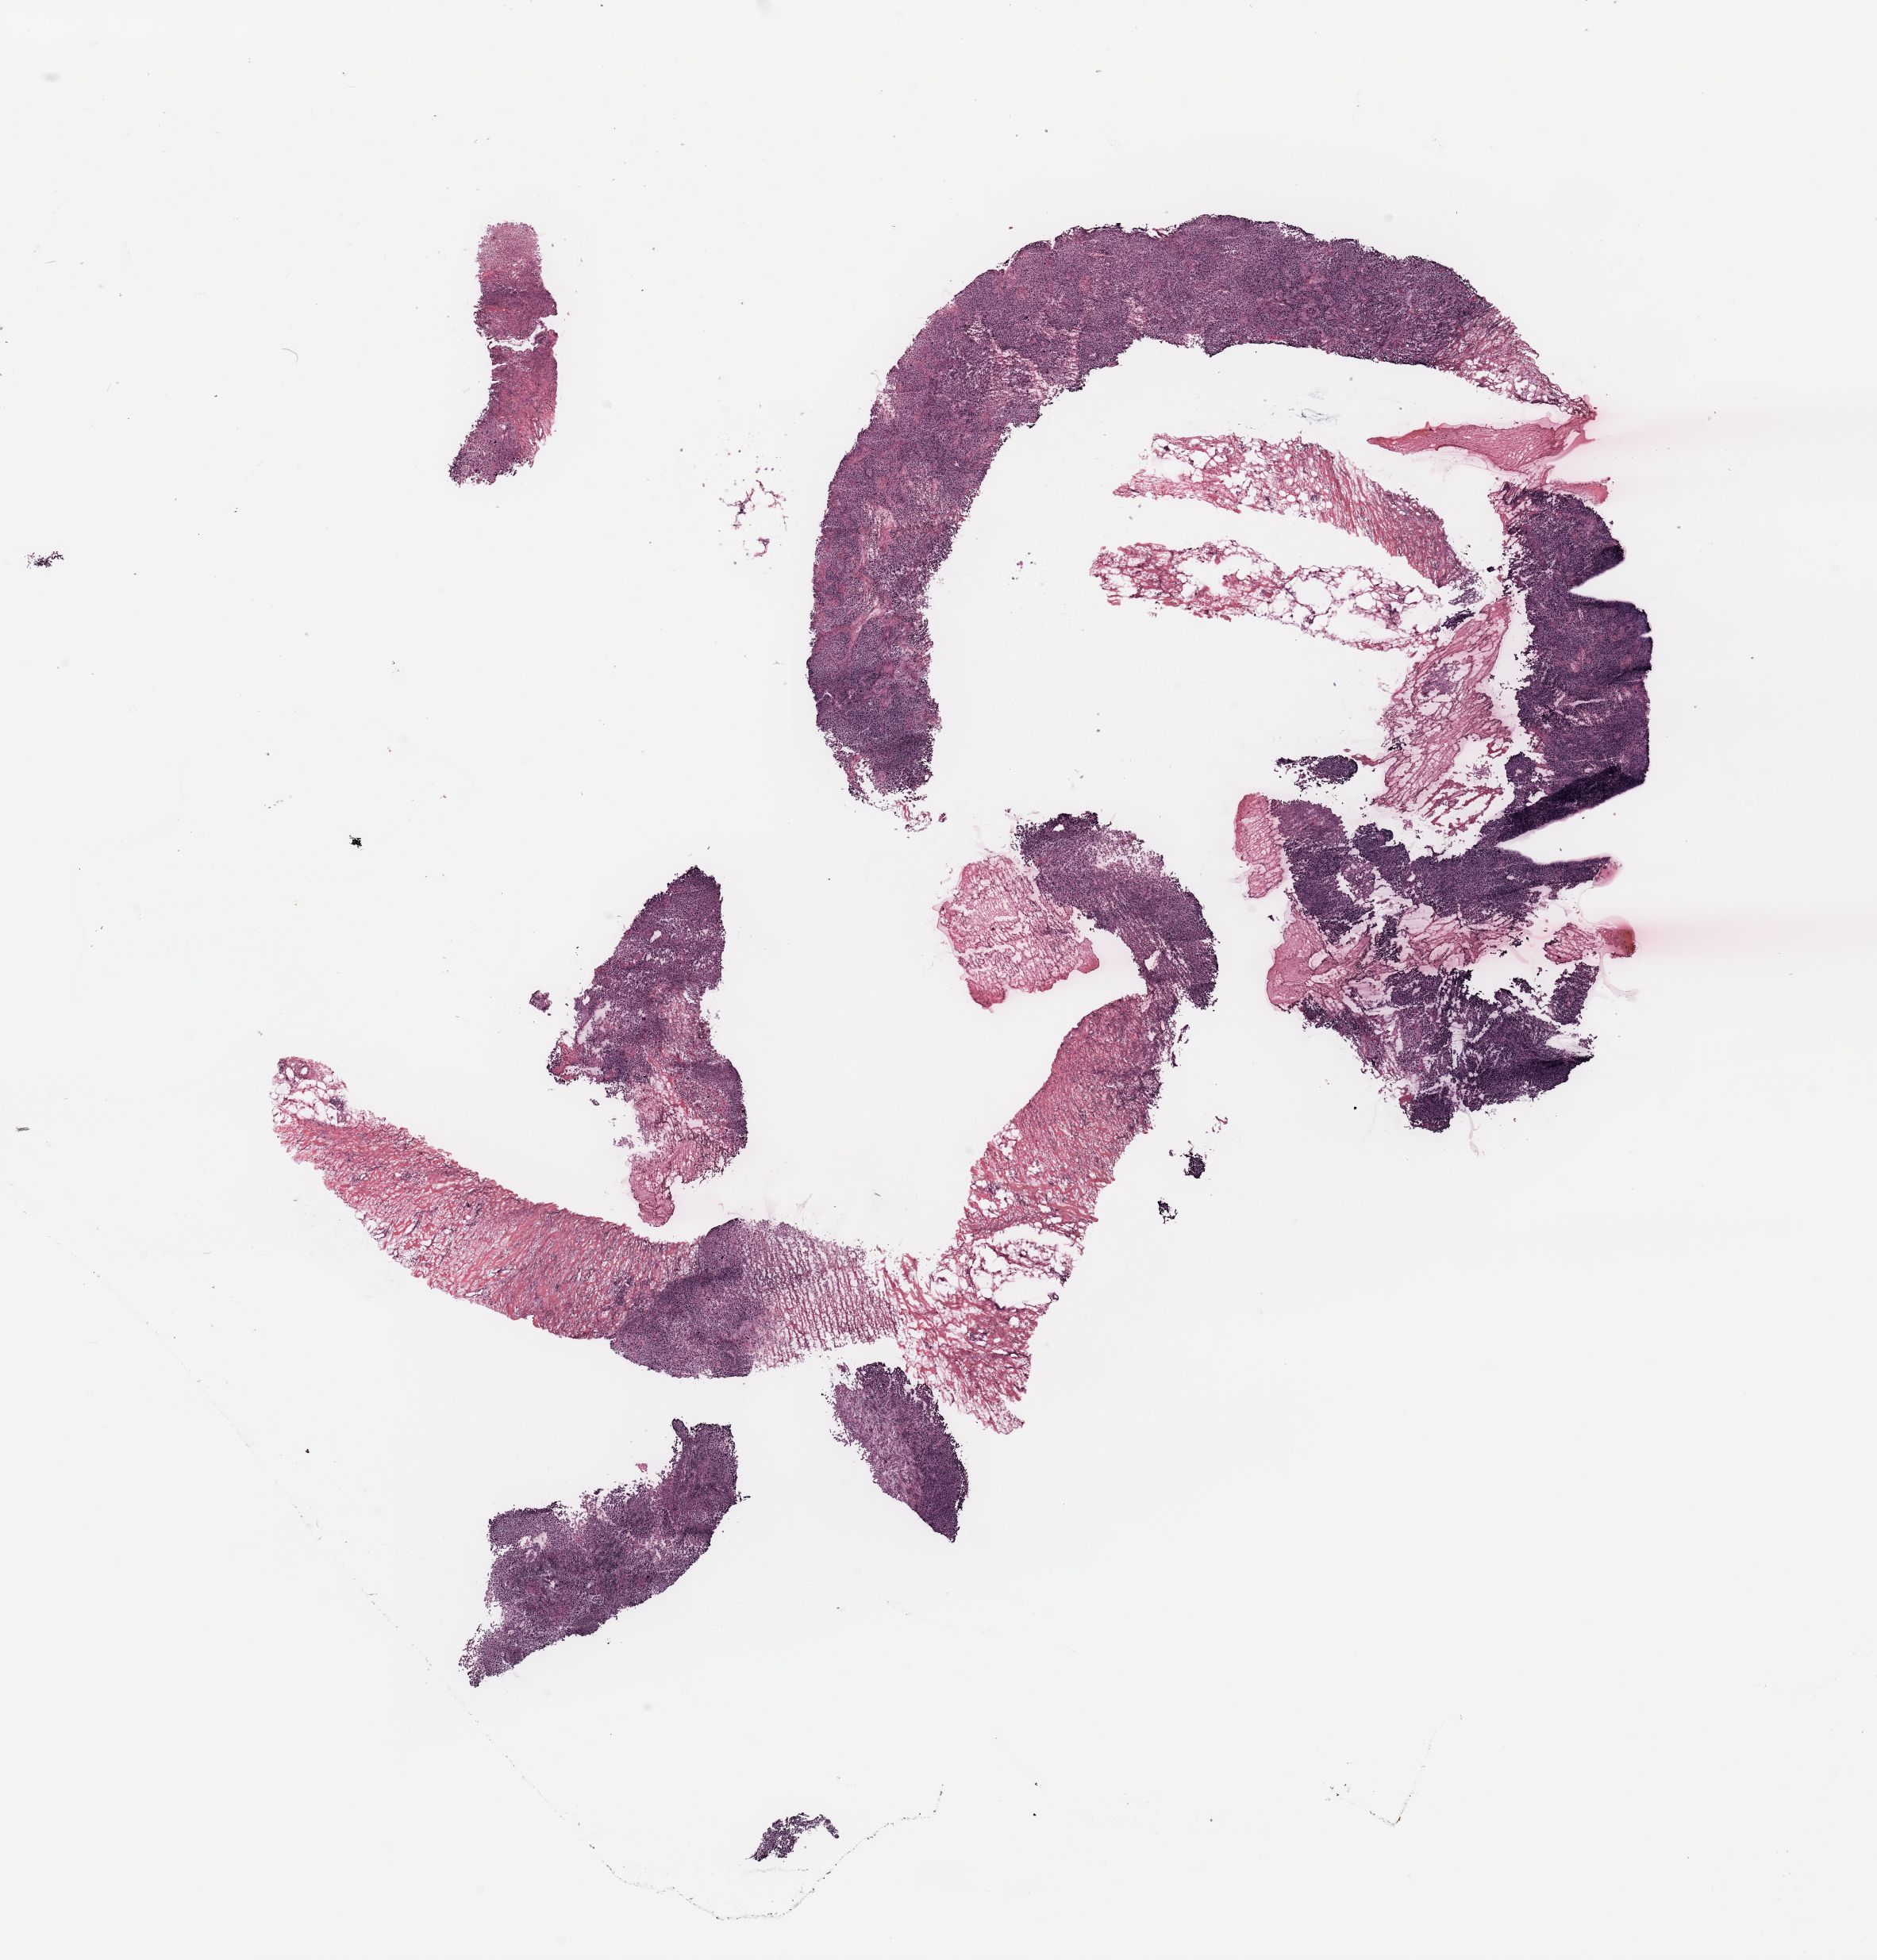
H&E-stained whole-slide image, a low-resolution overview of the entire scanned area, about 18.7 x 19.5 mm (acquisition: 20x scan), breast, tumour tissue. 59-year-old female patient.
Diagnosis: Adenocarcinoma, NOS. AJCC pathologic stage: II.